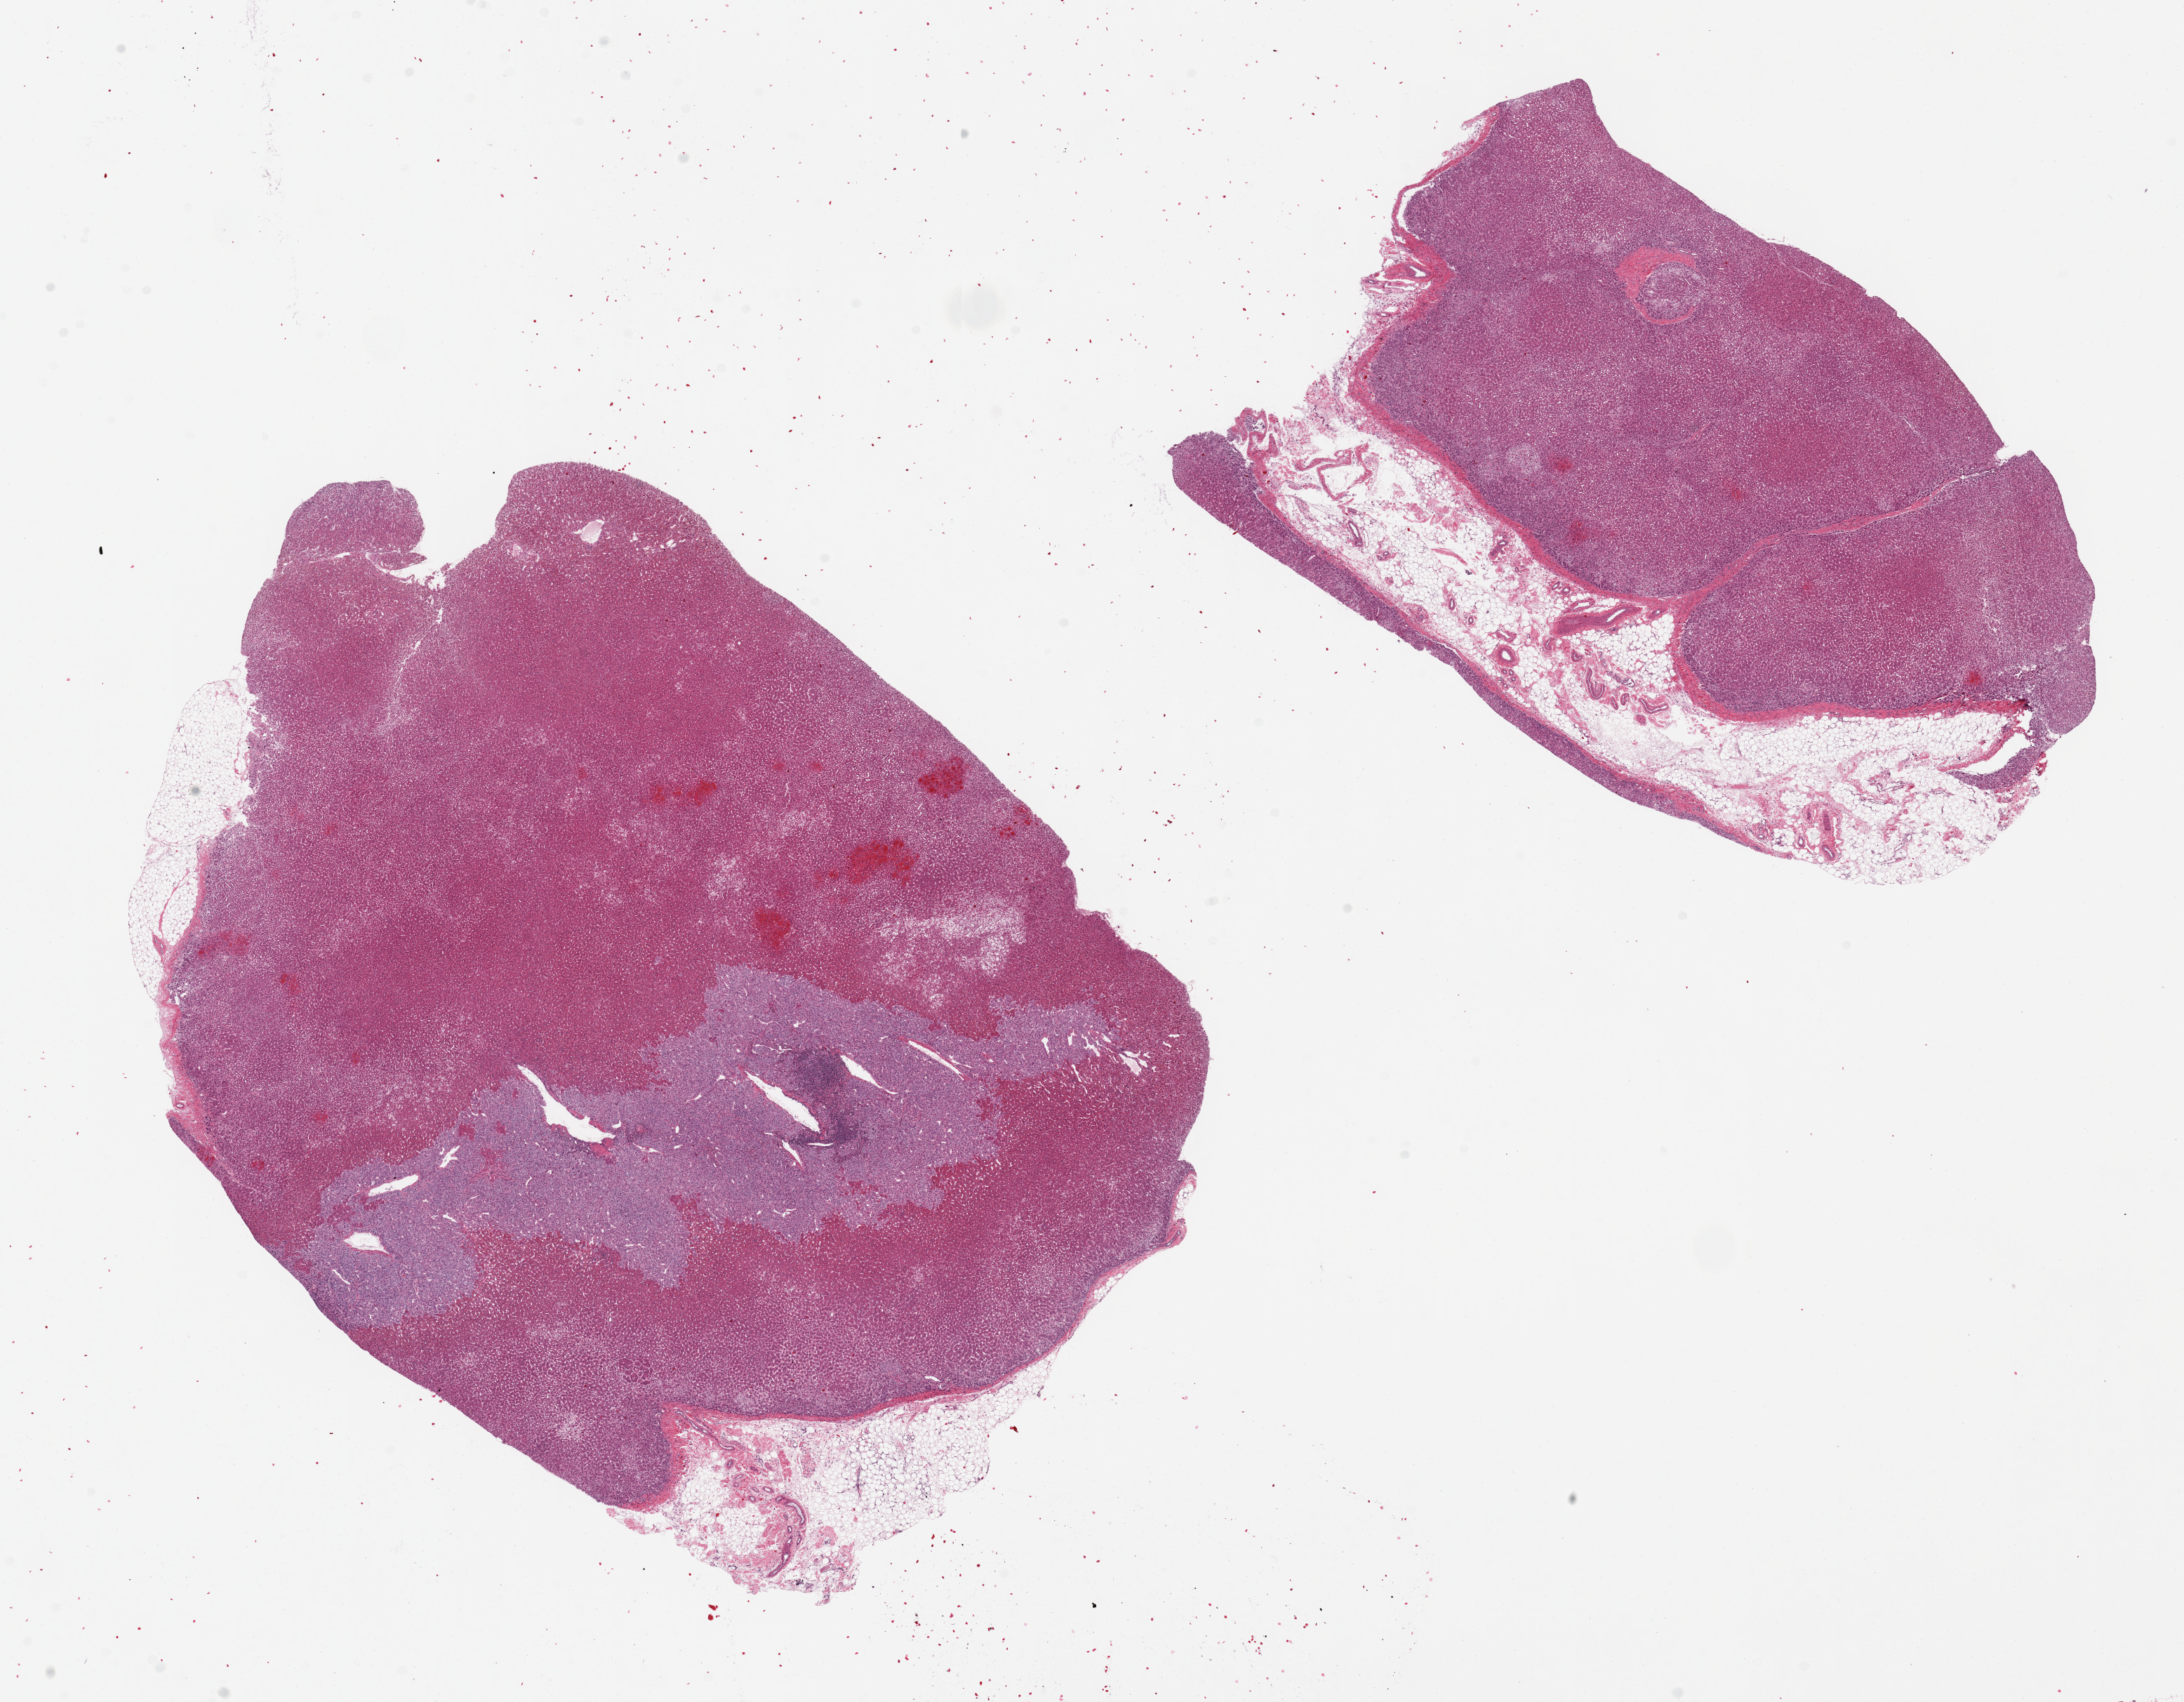
Whole-slide image, hematoxylin and eosin (H&E) stain, low-resolution overview of the scanned area, about 24.6 x 19.2 mm; PAXgene-fixed, paraffin-embedded tissue; section of adrenal gland (target tissue); donor tissue sample.
• reviewer comment on this tissue sample: 2 pieces. 13x10 & 10x6.5mm; 1 with cortex and medulla & 10% adipose. other with 30% internal adipose